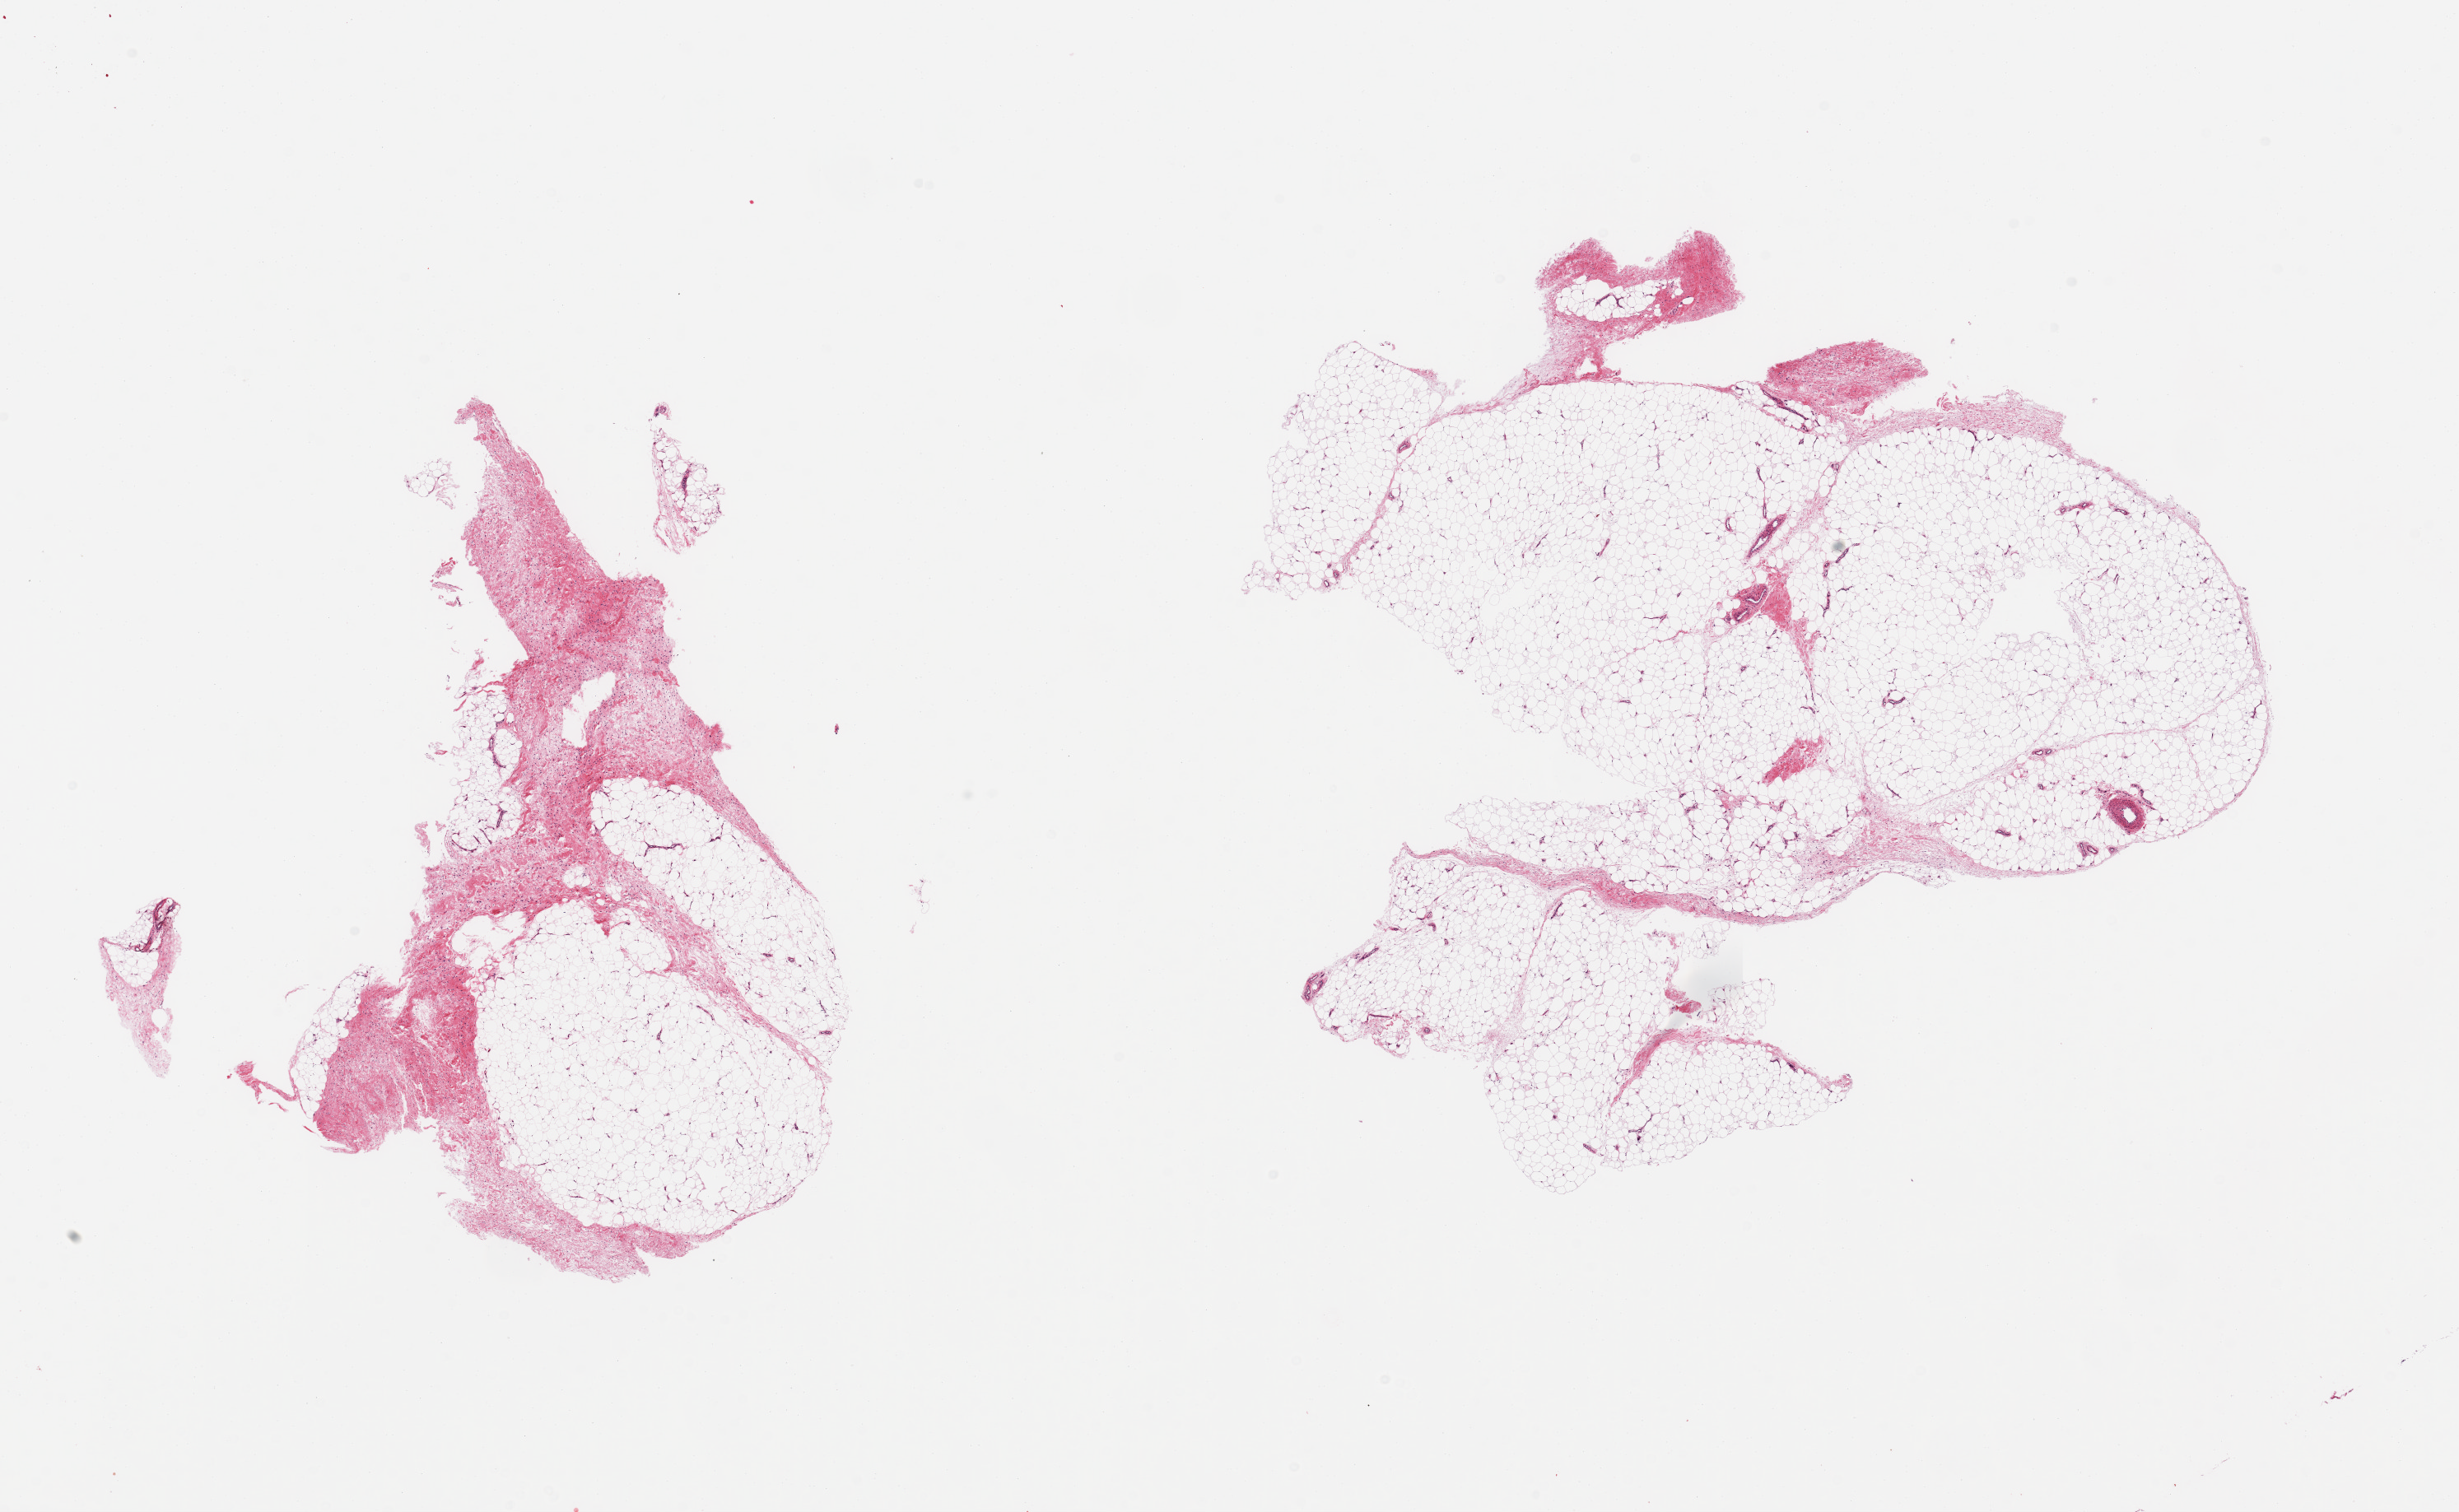
Hematoxylin and eosin (H&E) whole-slide image, brightfield — low-resolution overview of the scanned area, about 23.6 x 14.5 mm, PAXgene-fixed paraffin-embedded (PFPE) section, sampled site (target tissue): adipose tissue, tissue donor sample.
Reviewer comment on this tissue sample: 2 pieces; 5 & 10% fibrous content.